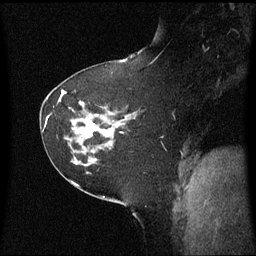
Breast MRI (dynamic contrast-enhanced), one sagittal slice; slice 35 of 60 in the series (ordered by position); dynamic contrast-enhanced series, image 2 of 3 at this slice position (ordered by acquisition); 1.5 T; TE 4.2 ms, TR 8.4 ms; 256 × 256 image matrix. Female patient, age 60 years. From the clinical record (not read from this slice): setting: breast cancer imaged before/during neoadjuvant chemotherapy; receptor status: triple-negative.
Outlined on this slice (semi-automatically segmented with operator editing):
- analysis volume of interest (the breast-tissue region the enhancement analysis was run in; not a lesion): box from (x=64, y=102) to (x=128, y=161) px
- tumour enhancement mask (voxels above the 70 % enhancement threshold inside the analysis volume of interest): (x=89, y=124)–(x=97, y=133)